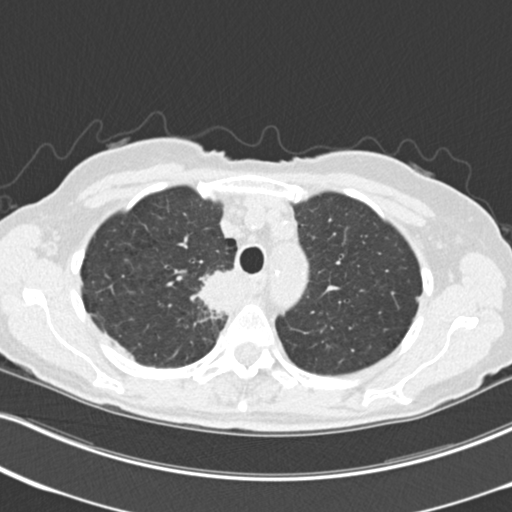
Axial slice from a low-dose chest CT screening exam, third annual screen, lung window (W 1500 / L -600 HU), 2 mm slice thickness, slice 52 of 226 in the series, 512 × 512 image matrix. Female participant, aged 68 years at enrolment. Current smoker at enrolment.
Expert-annotated lung lesion, bounding box [x1, y1, x2, y2] px = [198, 265, 250, 320]. Reader record for this screening exam (exam-level; its link to the box is not recorded): non-calcified nodule or mass ≥4 mm, right upper lobe, 31 × 29 mm, poorly defined margins, soft tissue attenuation, pre-existing on the prior screen: no. Official screen result: positive, other. Participant outcome: lung cancer diagnosed 79 days after this screen — squamous cell carcinoma, NOS, right upper lobe, mediastinum, poorly differentiated (G3), stage IIIB (AJCC 6th edition), 43 mm at pathology.